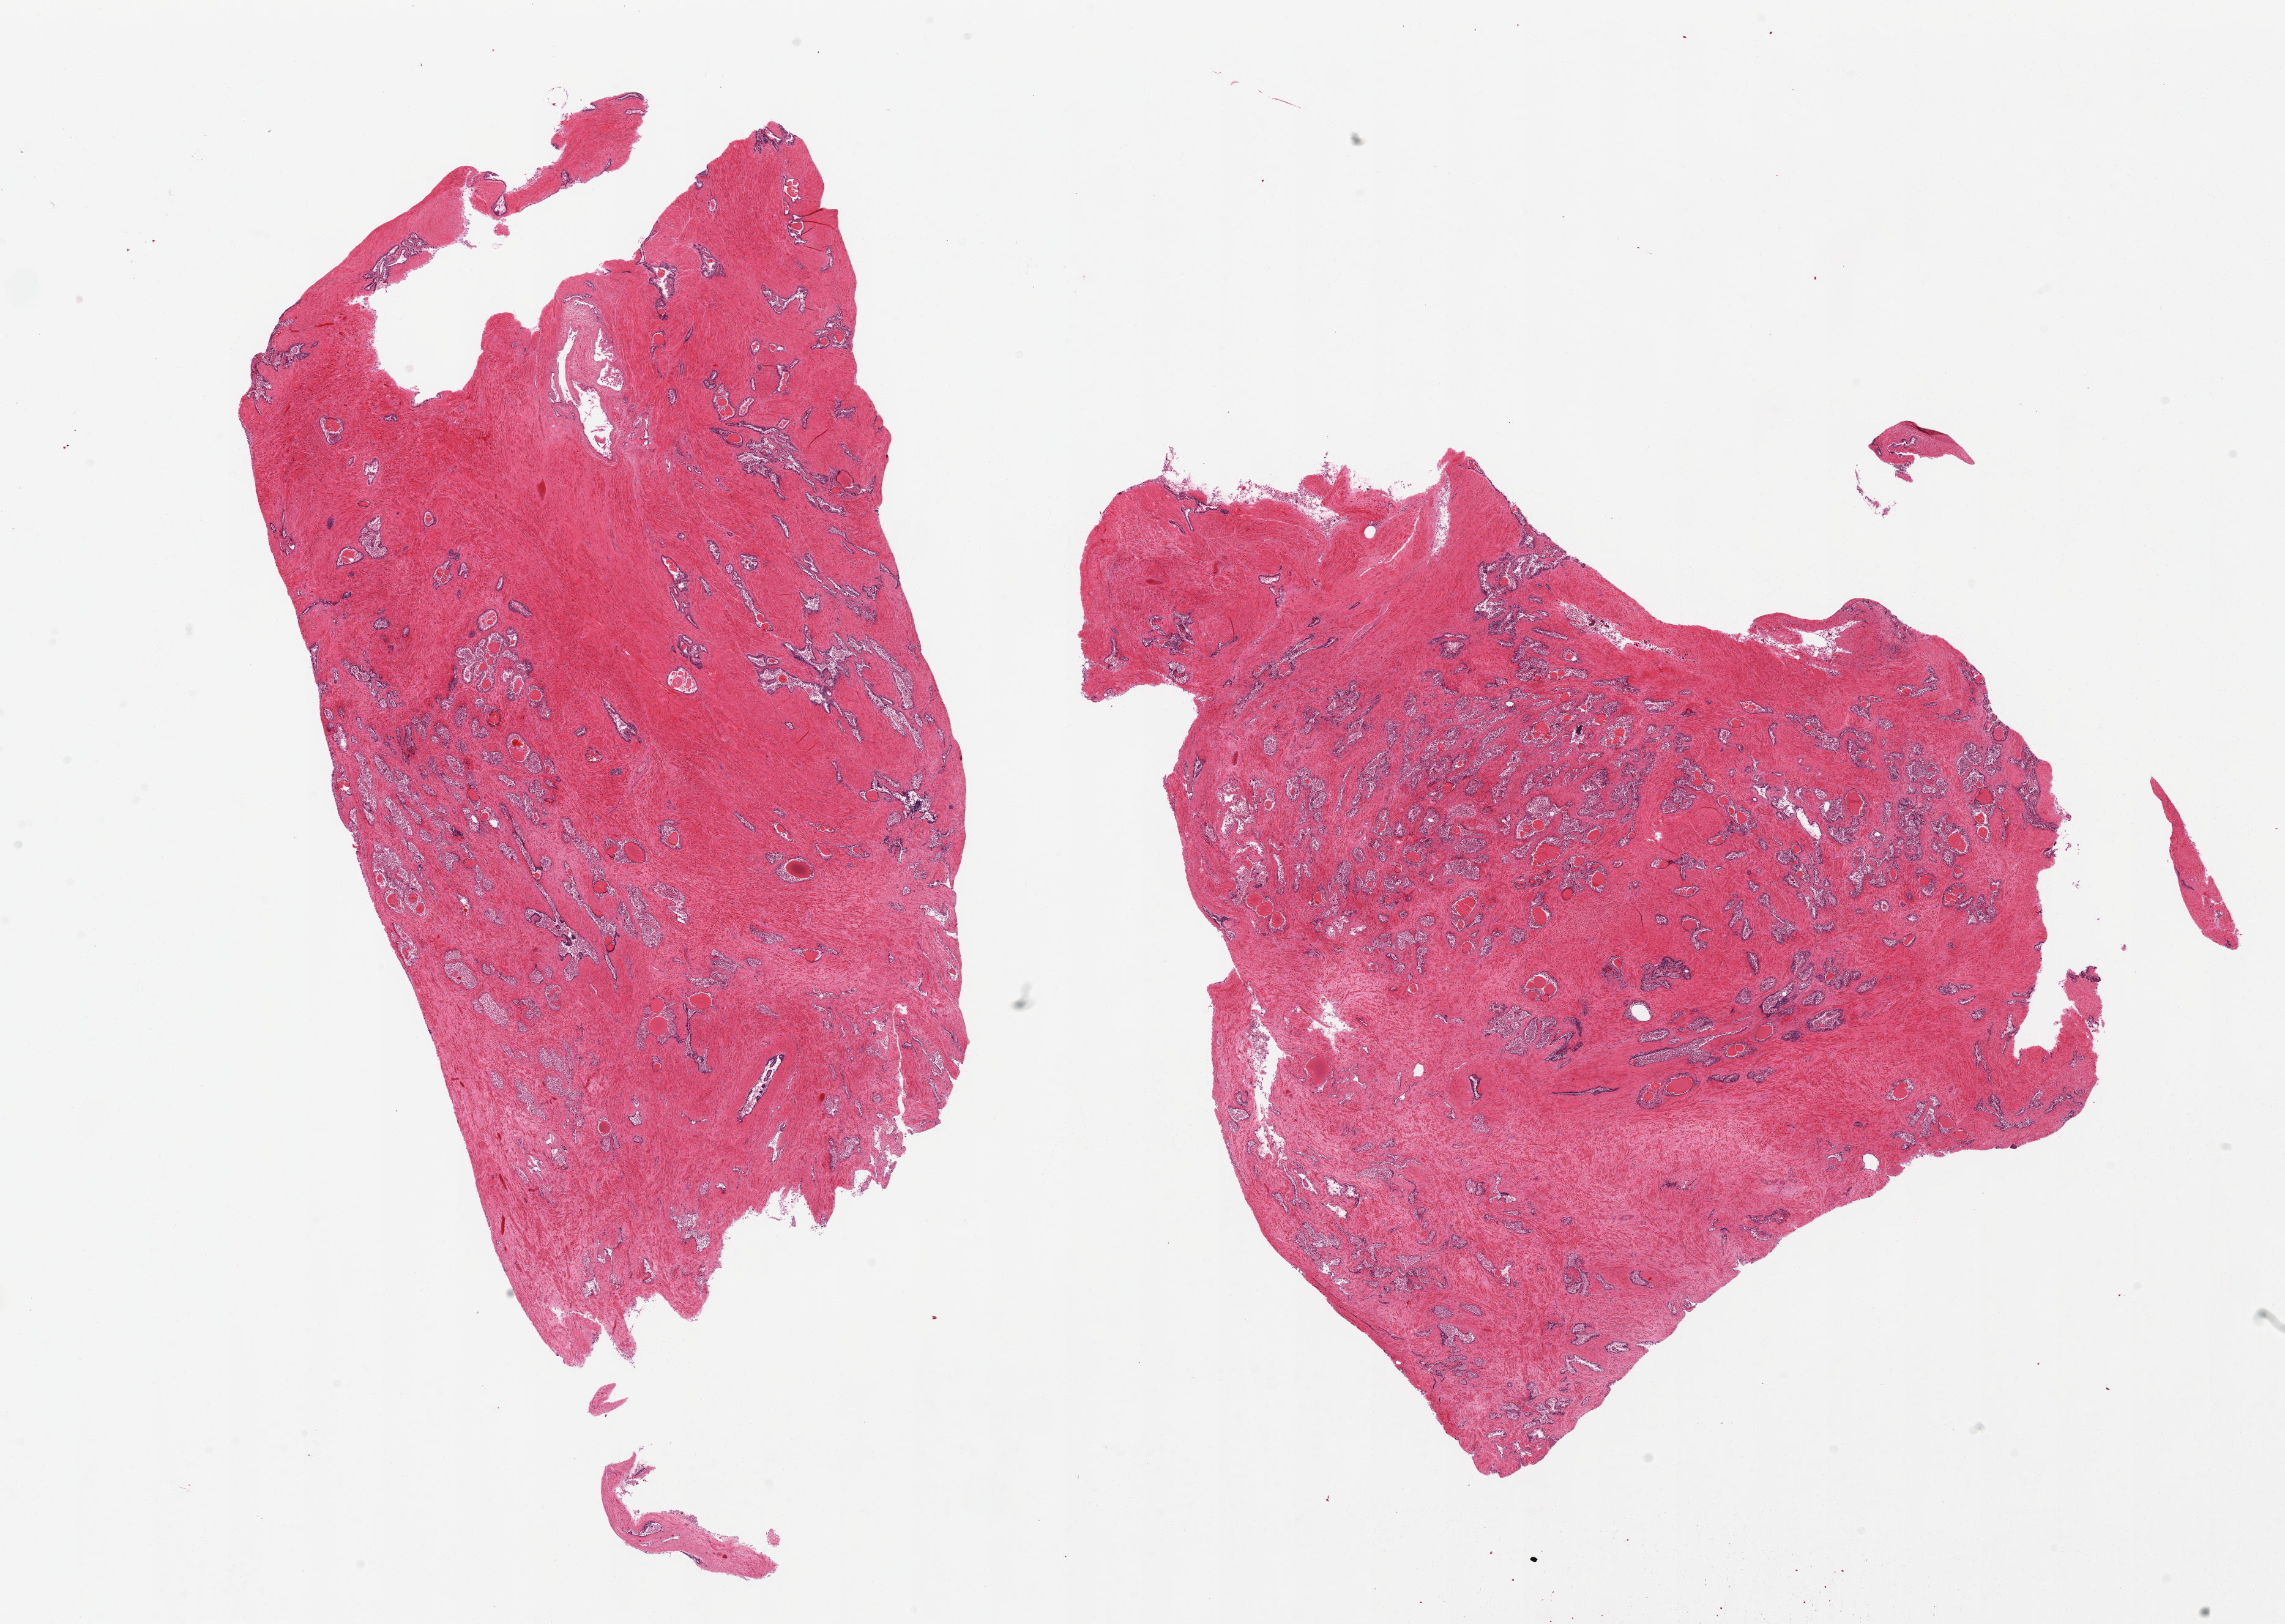
H&E whole-slide image, whole scanned area (about 29.5 x 21.0 mm, from a 20x scan) shown as a low-resolution overview. PAXgene-fixed, paraffin-embedded tissue. Sampled site (target tissue): prostate. Tissue donor sample. Donor: male.
Reviewer comment on this tissue sample: 2 pieces, glandular epithelial elements markedly autolyzed, hyperplastic pattern.